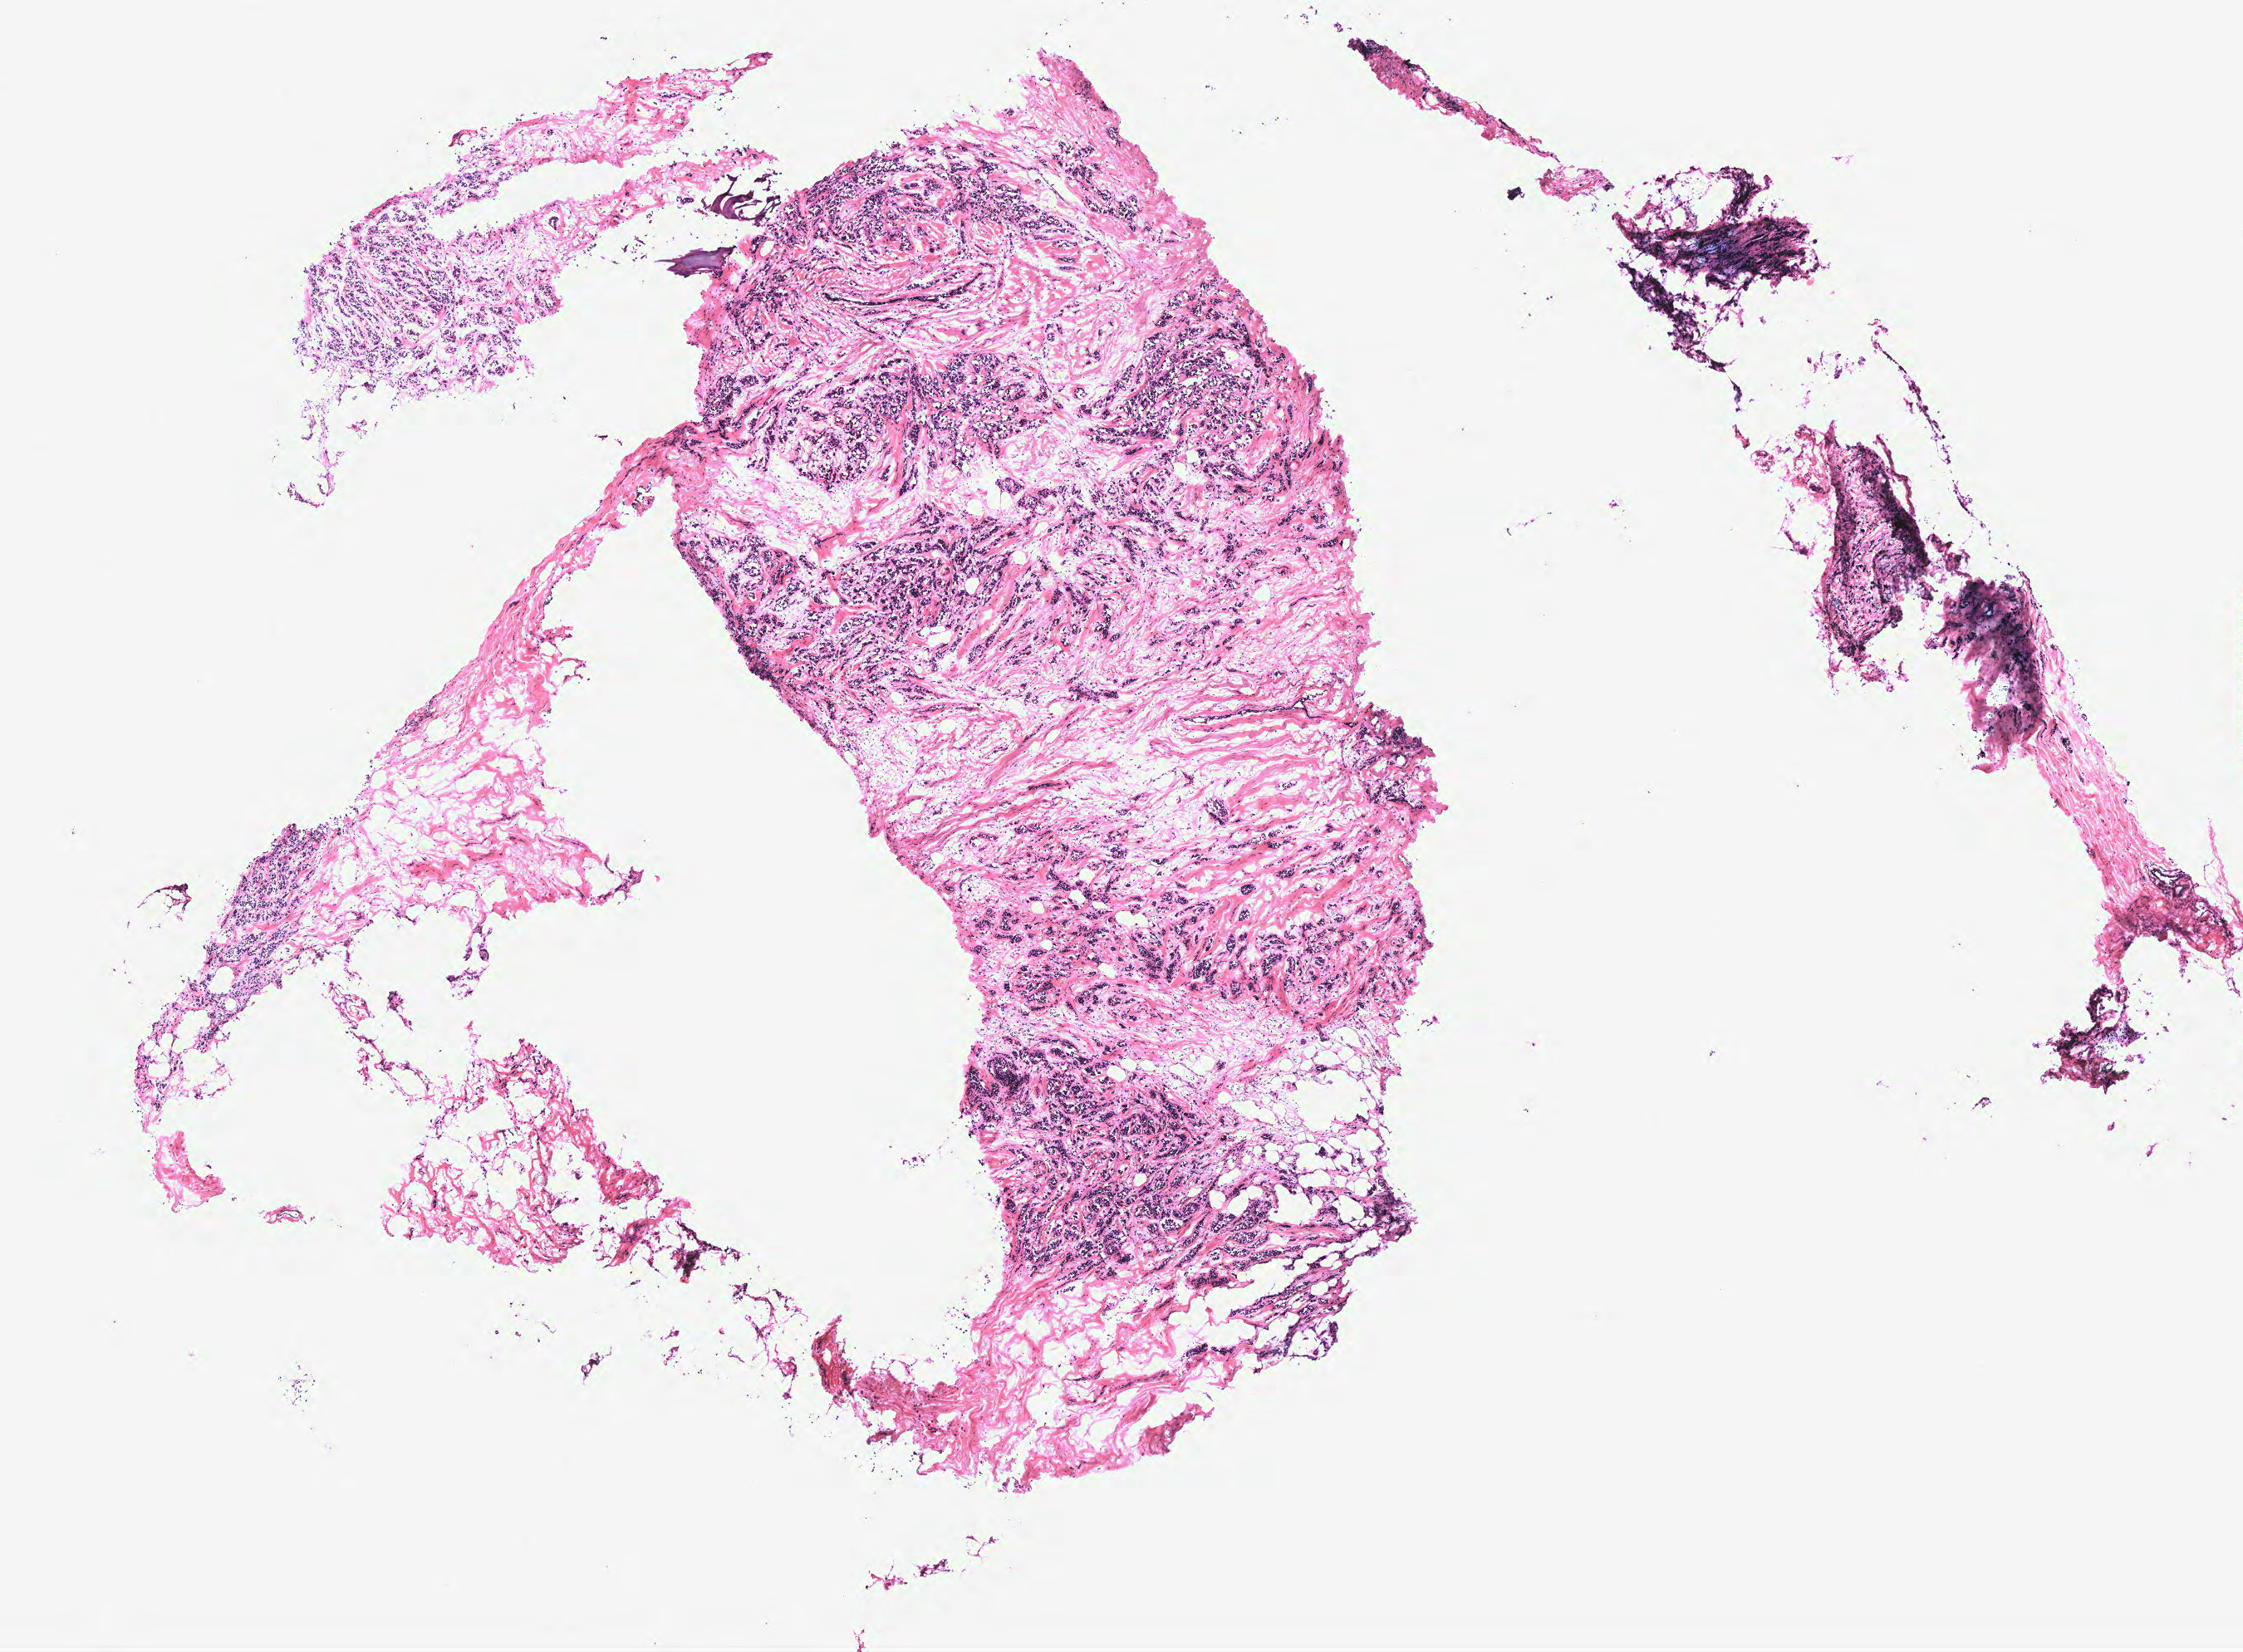
Digitized H&E tissue section (whole slide), a low-resolution overview of the entire scanned area, about 10.8 x 8.0 mm; breast, tissue type not recorded.
• patient diagnosis (cohort enrolment): breast cancer (breast)